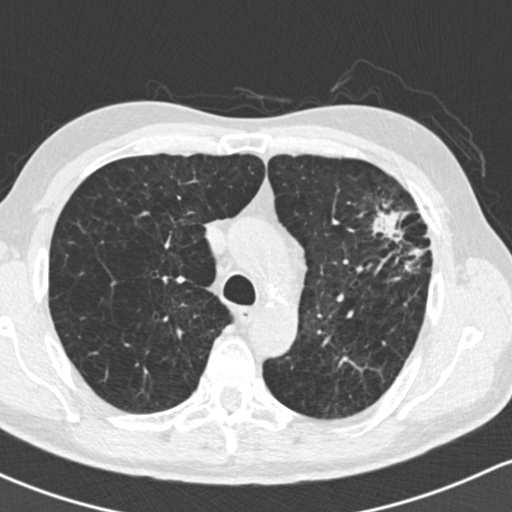
Axial slice from a low-dose chest CT screening exam; first (baseline) screen; lung window (W 1500 / L -600 HU); standard (soft-tissue) reconstruction kernel (B30f); slice 52 of 162 in the series. Male, age 61 years at enrolment. Former smoker at enrolment.
• Expert reader's lesion annotation, bounding box [x1, y1, x2, y2] px = [353, 184, 446, 289].
• Screening reader's record for this exam (one nodule recorded; not confirmed to be the boxed lesion): non-calcified nodule or mass ≥4 mm, left upper lobe, 35 × 35 mm, spiculated (stellate) margins, soft tissue attenuation.
• Official screen result: positive, change unspecified: nodule(s) >= 4 mm or enlarging nodule(s), mass(es), or other non-specific abnormalities suspicious for lung cancer.
• Later outcome: lung cancer diagnosed 19 days after this screen — adenocarcinoma, NOS, left upper lobe, well differentiated (G1), stage IIIA (AJCC 6th edition), 45 mm at pathology.